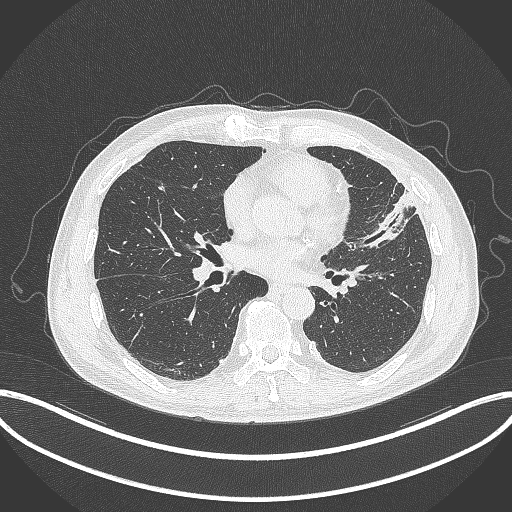
Chest CT, one axial slice. Position 153 of 382 along the scan axis. Lung window (W 1500 / L -600 HU). 512 × 512 image matrix. Patient: male, 64 years. From the clinical record (not read from this slice): clinical TNM (as recorded): T4 N1 M0; histopathological grade: G3.
Structures marked on this image (rectangle marked by the reading radiologist):
- lung tumour (recorded histology: adenocarcinoma): box from (x=361, y=188) to (x=419, y=252) px